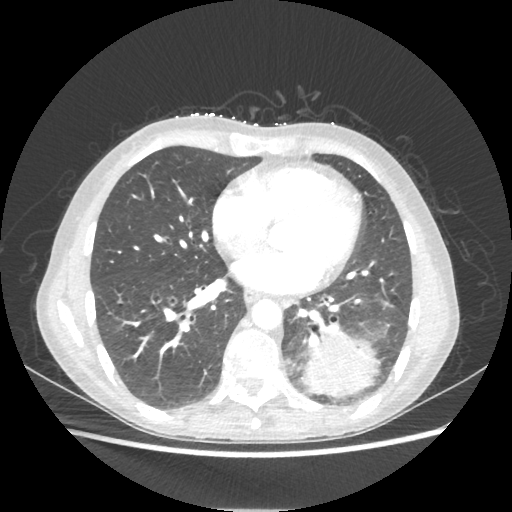
Chest CT, one axial slice. Slice 89 of 221 in the series (ordered by position). Lung window (W 1500 / L -600 HU). 512 × 512 image matrix. Patient: female, 53 years. Case-level facts recorded for this patient, not image findings: clinical TNM (as recorded): T3 N0 M0.
Structures marked on this image (rectangle marked by the reading radiologist):
- lung tumour (recorded histology: adenocarcinoma): bounding box <301,329,380,397> (left, top, right, bottom; pixels)